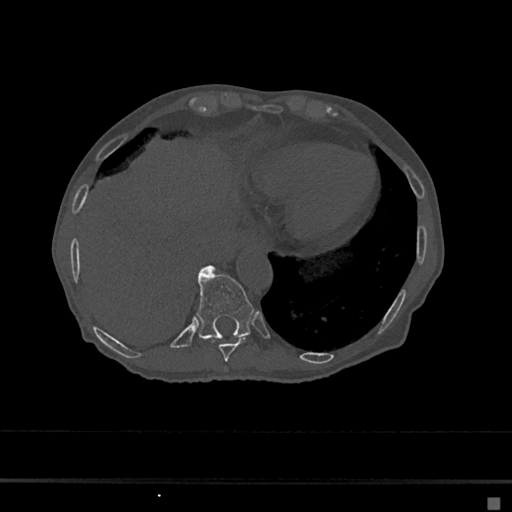
CT including the spine, one axial slice. Reconstruction kernel Br40s/3. Bone window (W 1800 / L 400 HU). 512 × 512 image matrix. Patient: female, 68 years. From the clinical record (not read from this slice): primary cancer: renal.
Outlined on this slice (semi-automatically segmented with operator editing):
- T10 vertebra: bounding box [x1, y1, x2, y2] px = [197, 266, 254, 339]
- T9 vertebra: [218, 337, 247, 362]